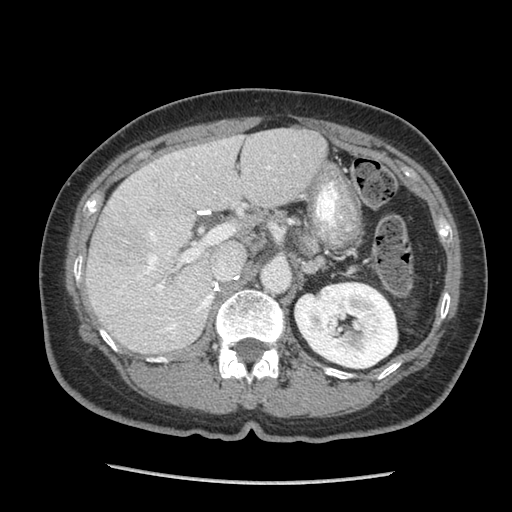
Contrast-enhanced abdominal CT (liver protocol), one axial slice; position 46 of 105 along the scan axis; 140 kVp; soft-tissue window (W 400 / L 40 HU); 2.5 mm slice thickness; 512 × 512 image matrix, field of view 340 × 340 mm. Case-level facts recorded for this patient, not image findings: diagnosis: hepatocellular carcinoma (patient treated with transarterial chemoembolisation; whether this scan precedes or follows treatment is not stated here); TNM stage (as recorded): Stage-I; Child-Pugh class: A; tumour differentiation: moderately differentiated; tumour nodularity: uninodular.
Annotated regions visible in this slice (semi-automatic segmentation, software-assisted and operator-edited):
- liver parenchyma outside the tumour (the mass and vessels are separate outlines, so this box may not span the whole liver): bounding box [x1, y1, x2, y2] px = [86, 128, 326, 352]
- mass: [91, 217, 145, 274]
- liver vessels: [123, 154, 271, 335]